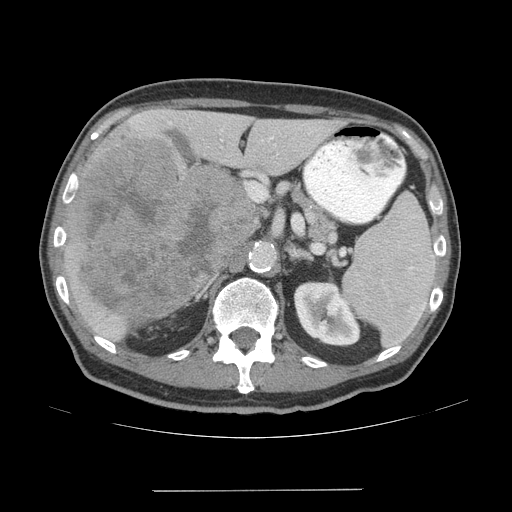
Contrast-enhanced abdominal CT (liver protocol), one axial slice; position 31 of 77 along the scan axis; 140 kVp; soft-tissue window (W 400 / L 40 HU); 2.5 mm slice thickness; 512 × 512 image matrix, field of view 400 × 400 mm. From the clinical record (not read from this slice): diagnosis: hepatocellular carcinoma (patient treated with transarterial chemoembolisation; whether this scan precedes or follows treatment is not stated here); TNM stage (as recorded): Stage-IVA; Child-Pugh class: A.
Outlined on this slice (semi-automatic segmentation, software-assisted and operator-edited):
- liver parenchyma outside the tumour (the mass and vessels are separate outlines, so this box may not span the whole liver): box from (x=64, y=108) to (x=345, y=340) px
- mass: (x=69, y=139)–(x=255, y=319)
- liver vessels: (x=169, y=122)–(x=273, y=140)